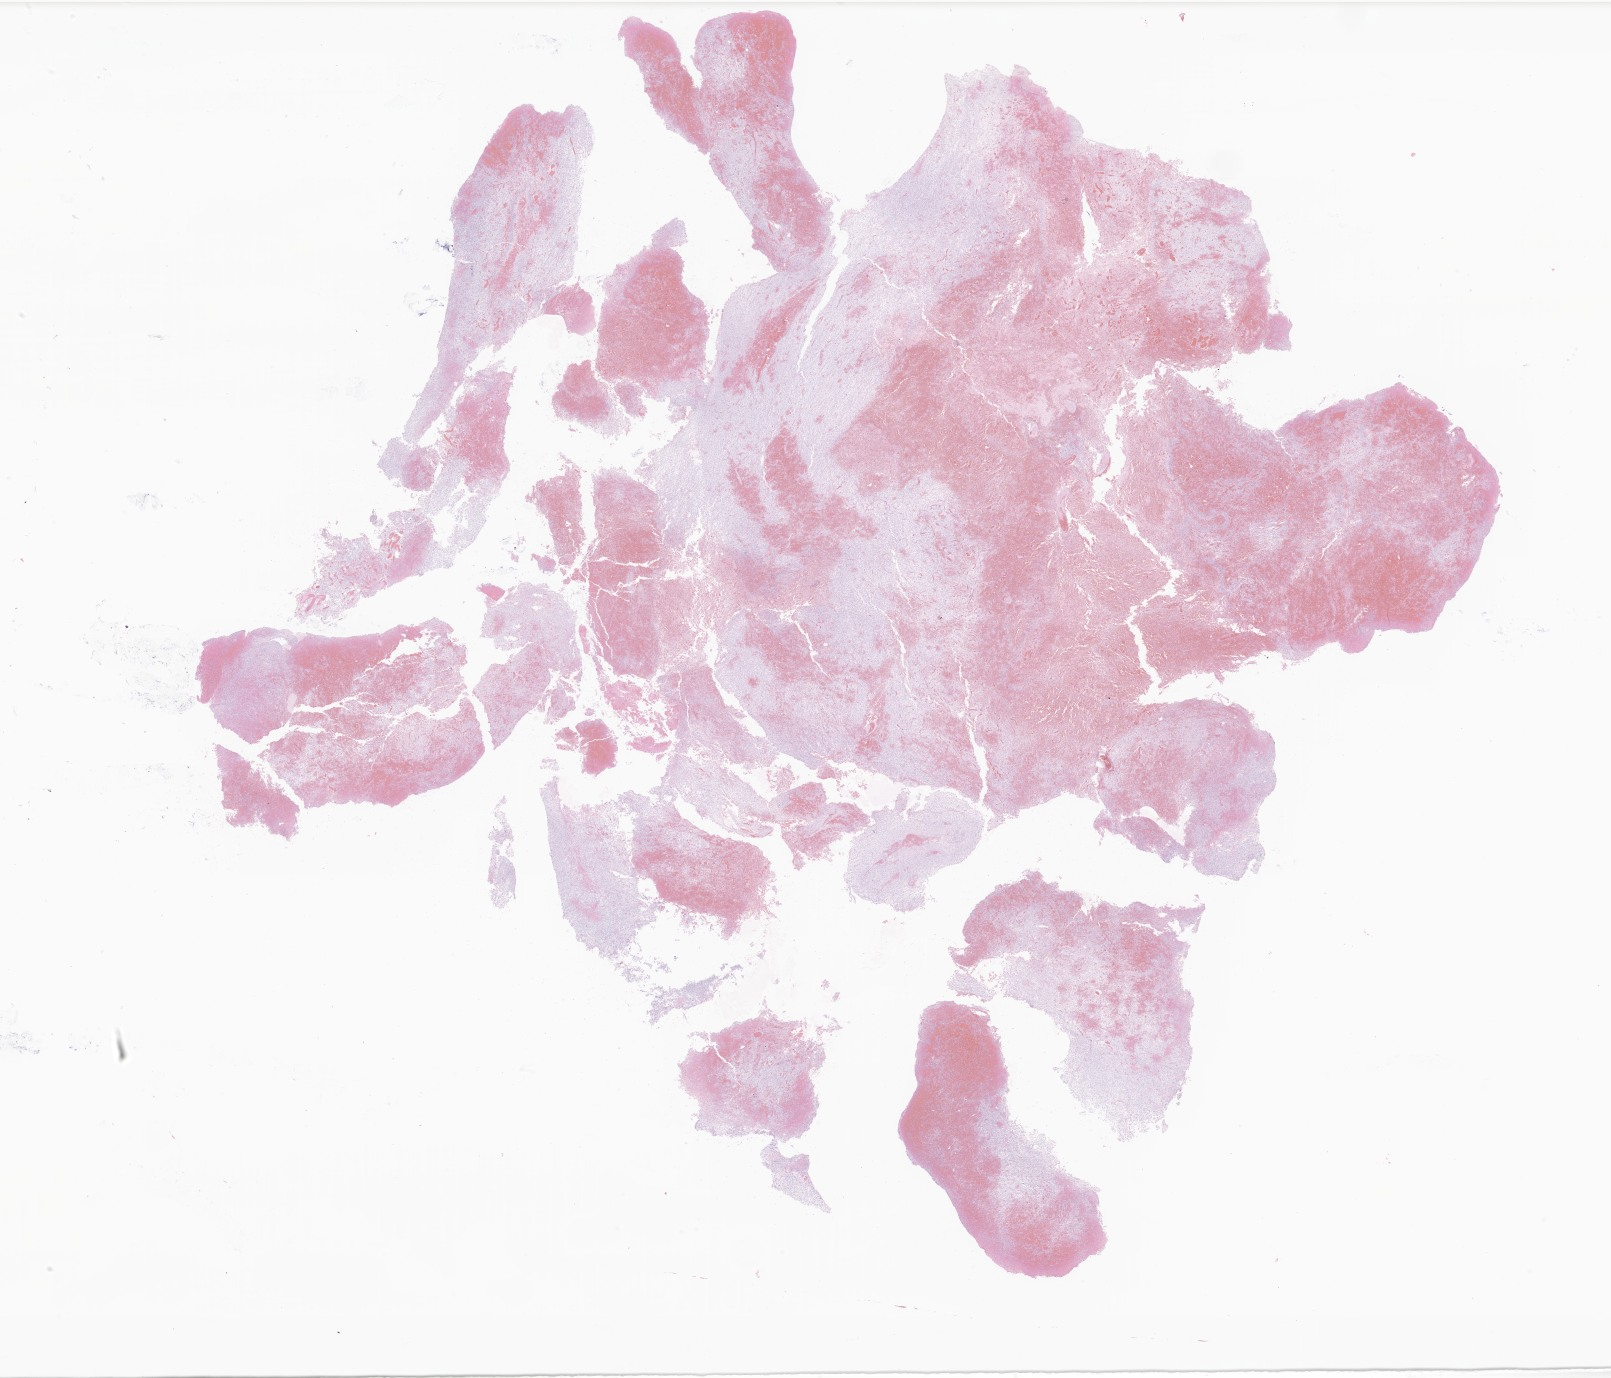
Whole-slide image, hematoxylin and eosin (H&E) stain of tumor tissue from the brain, low-resolution overview of the scanned area, about 27.2 x 23.2 mm, formalin-fixed paraffin-embedded section. Patient male; age 174 months (14 years 6 months).
Diagnosis: Glioma, malignant.